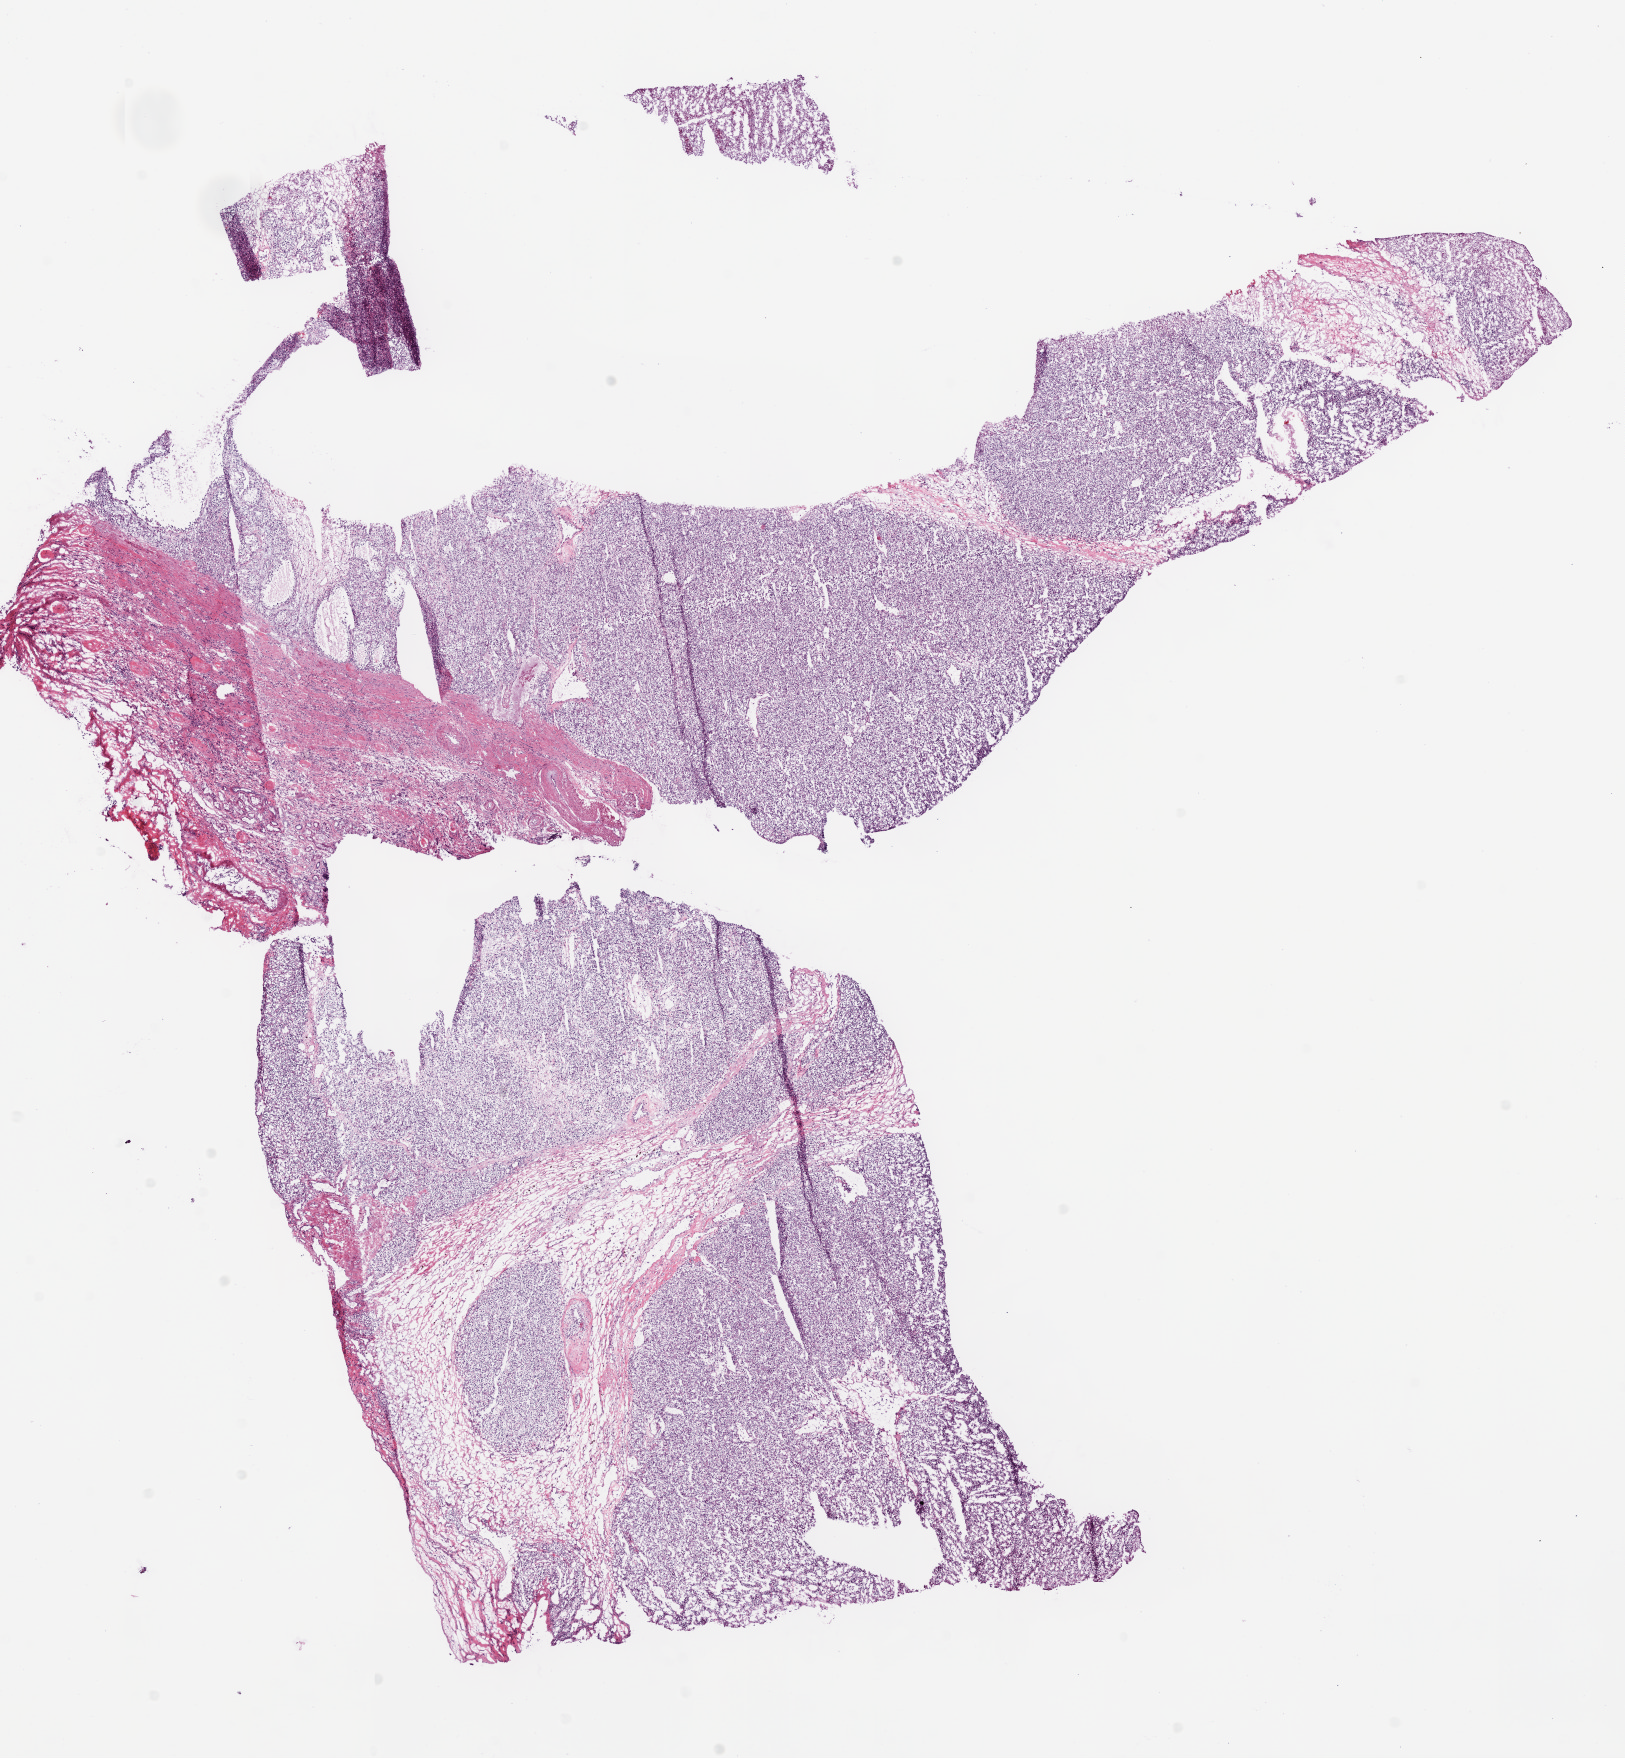
H&E-stained whole-slide image — whole scanned area (about 13.0 x 14.1 mm, from a 20x scan) shown as a low-resolution overview, frozen section, kidney, primary tumour sample. Male, age 72 years at initial diagnosis.
Pathologic diagnosis: Clear cell adenocarcinoma, NOS.